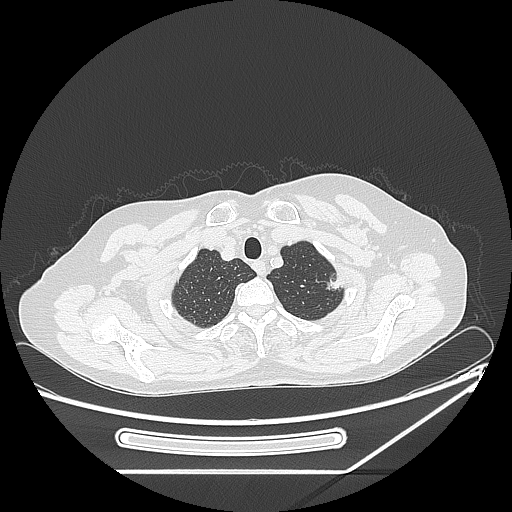
Chest CT, one axial slice. Position 214 of 250 along the scan axis. Reconstruction kernel LUNG. 120 kVp. Lung window (W 1500 / L -600 HU). 1.25 mm slice thickness. 512 × 512 image matrix, field of view 409 × 409 mm. Patient: female, 57 years. From the clinical record (not read from this slice): clinical TNM (as recorded): T1c N0 M0; histopathological grade: G2-3.
Structures marked on this image (bounding box drawn by a radiologist):
- lung tumour (recorded histology: adenocarcinoma): box from (x=317, y=270) to (x=340, y=295) px